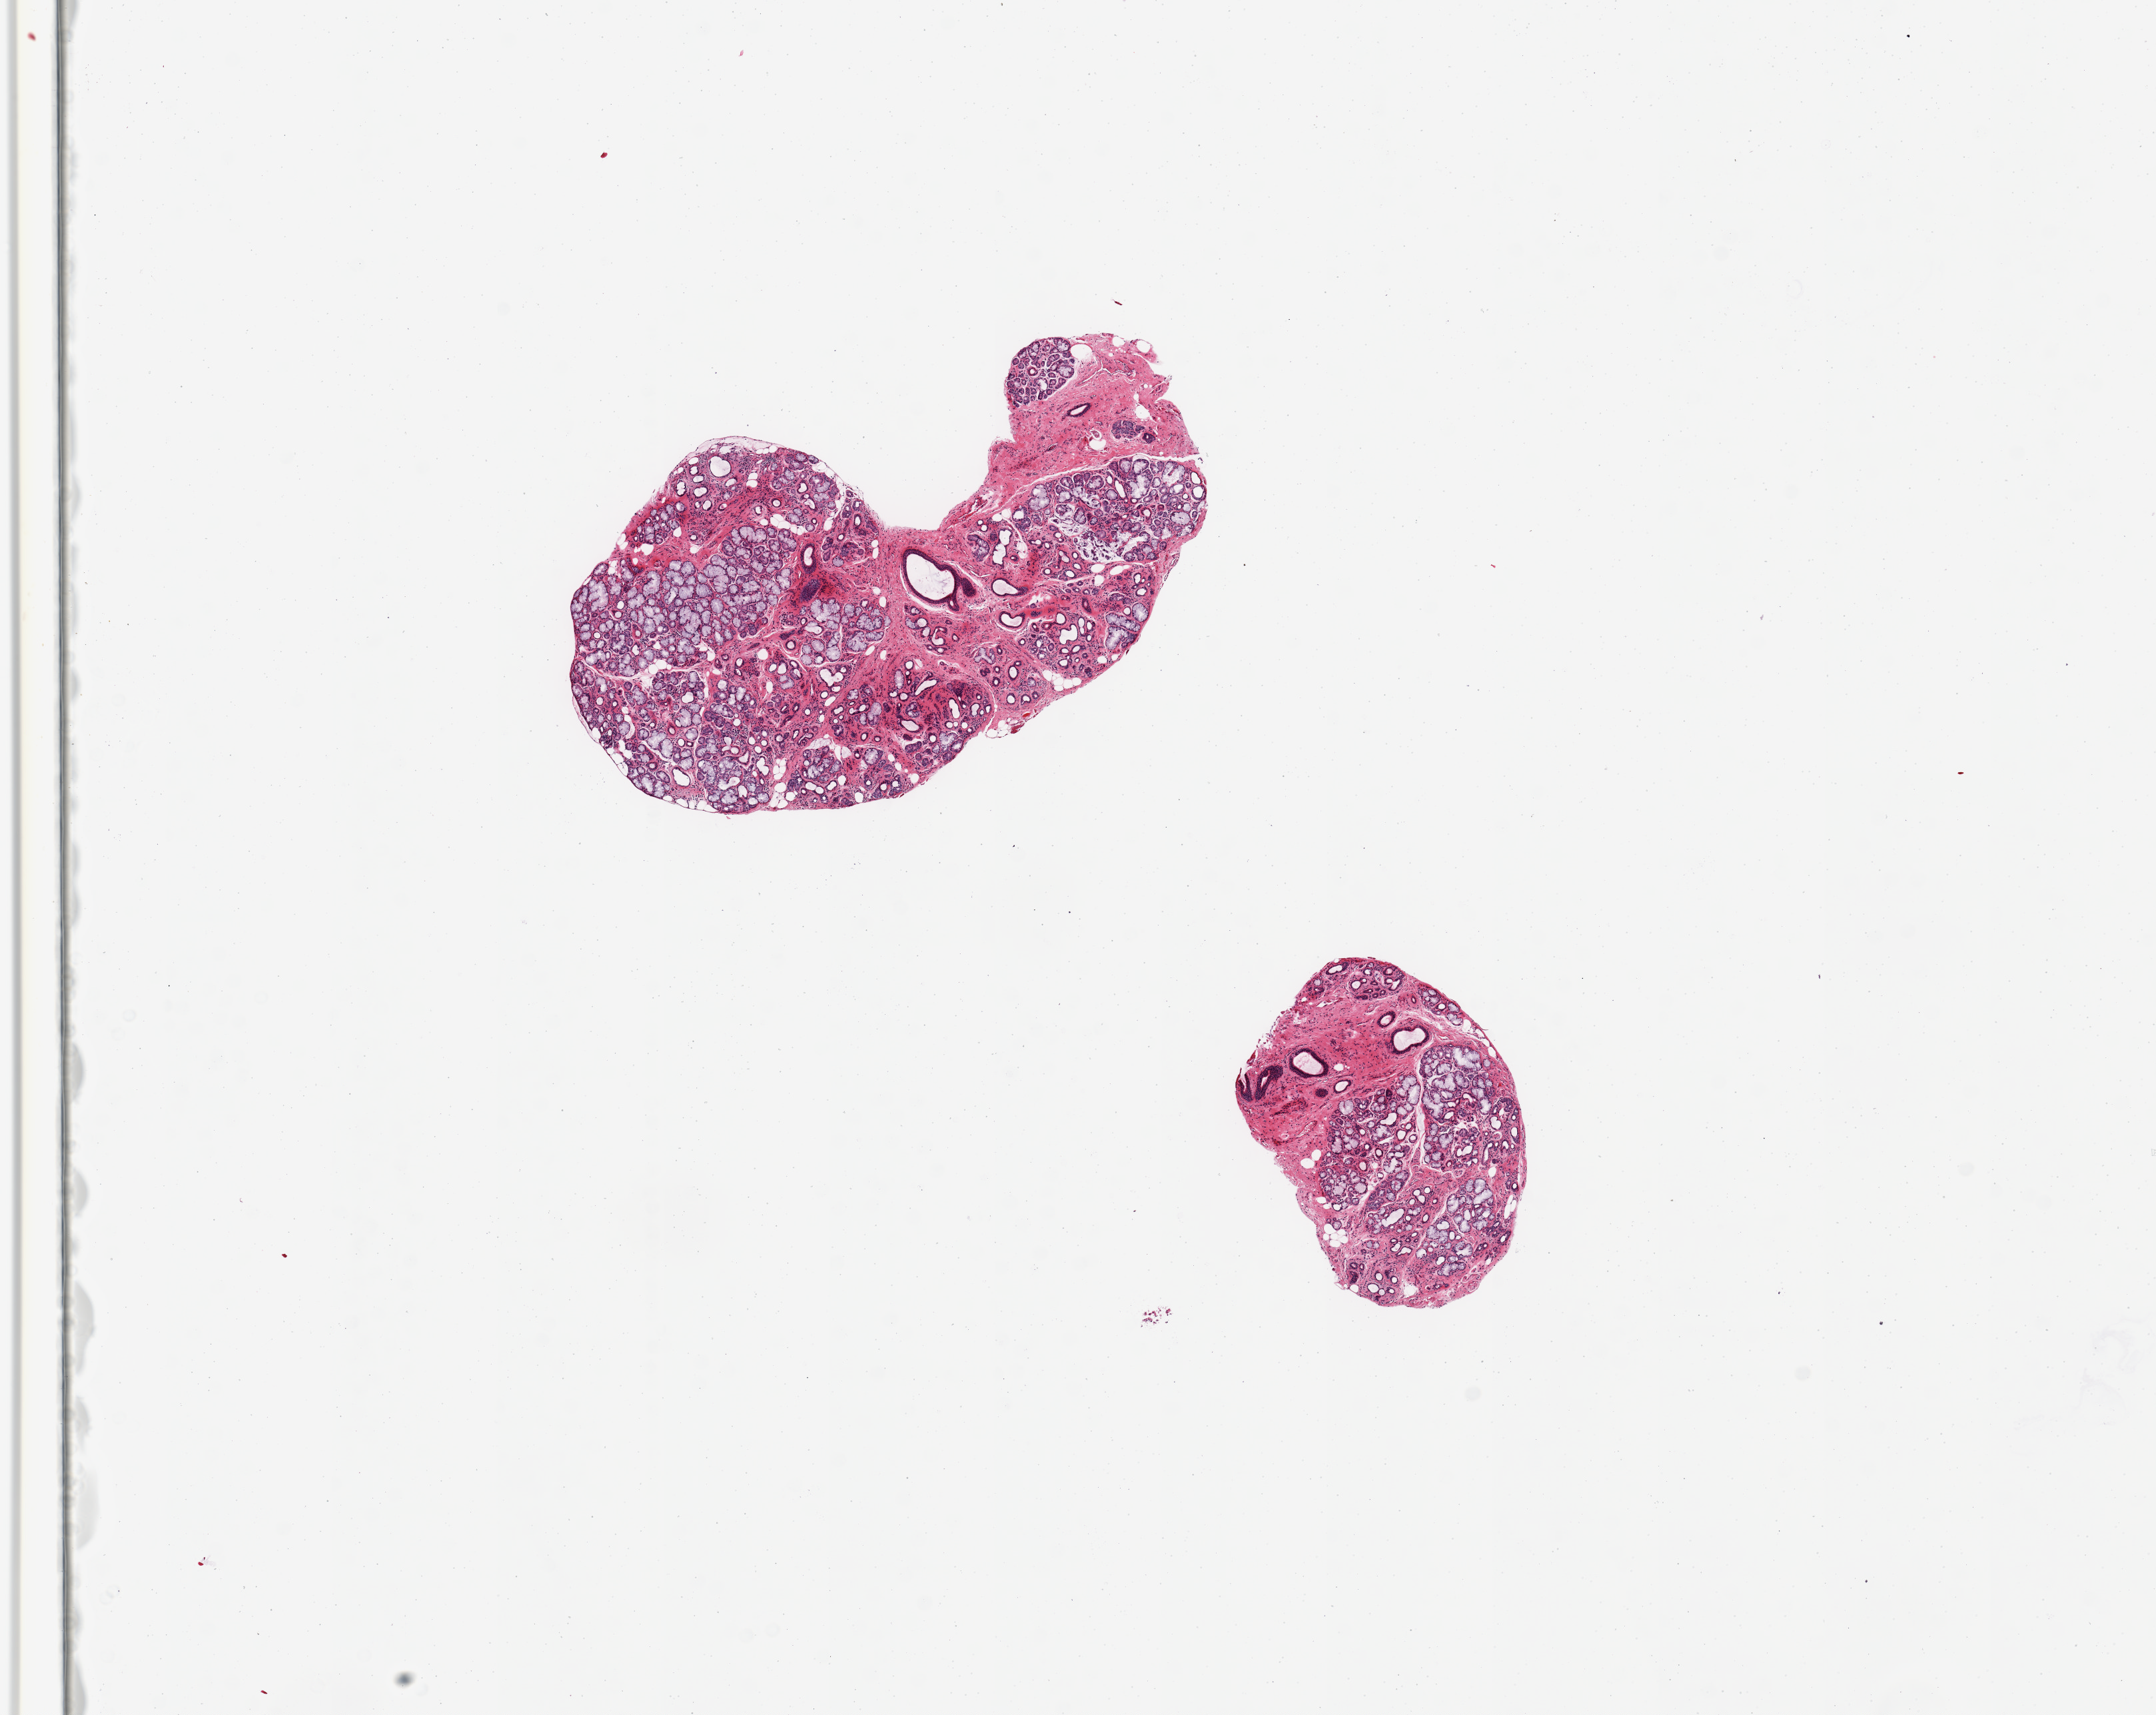
Haematoxylin and eosin whole-slide image, shown as a low-resolution overview of the whole scanned area (about 12.8 x 10.2 mm, from a 20x scan), PAXgene-fixed, paraffin-embedded tissue, sampled site (target tissue): minor salivary gland, donor tissue sample. Donor: male.
- pathologist's review note for this sample: 2 pieces, ~85% glandular elements; rest is stroma